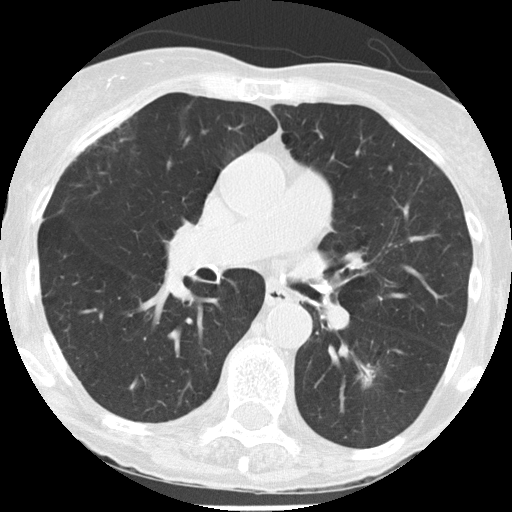
Low-dose screening chest CT, one axial slice; position 73 of 146 along the scan axis; 120 kVp; lung window (W 1500 / L -600 HU); 2 mm slice thickness; 512 × 512 image matrix, field of view 273 × 273 mm.
Annotated regions visible in this slice (manually delineated by an expert):
- lesion 1 (tumor, lower lobe of left lung): bounding box [x1, y1, x2, y2] px = [361, 364, 375, 385]